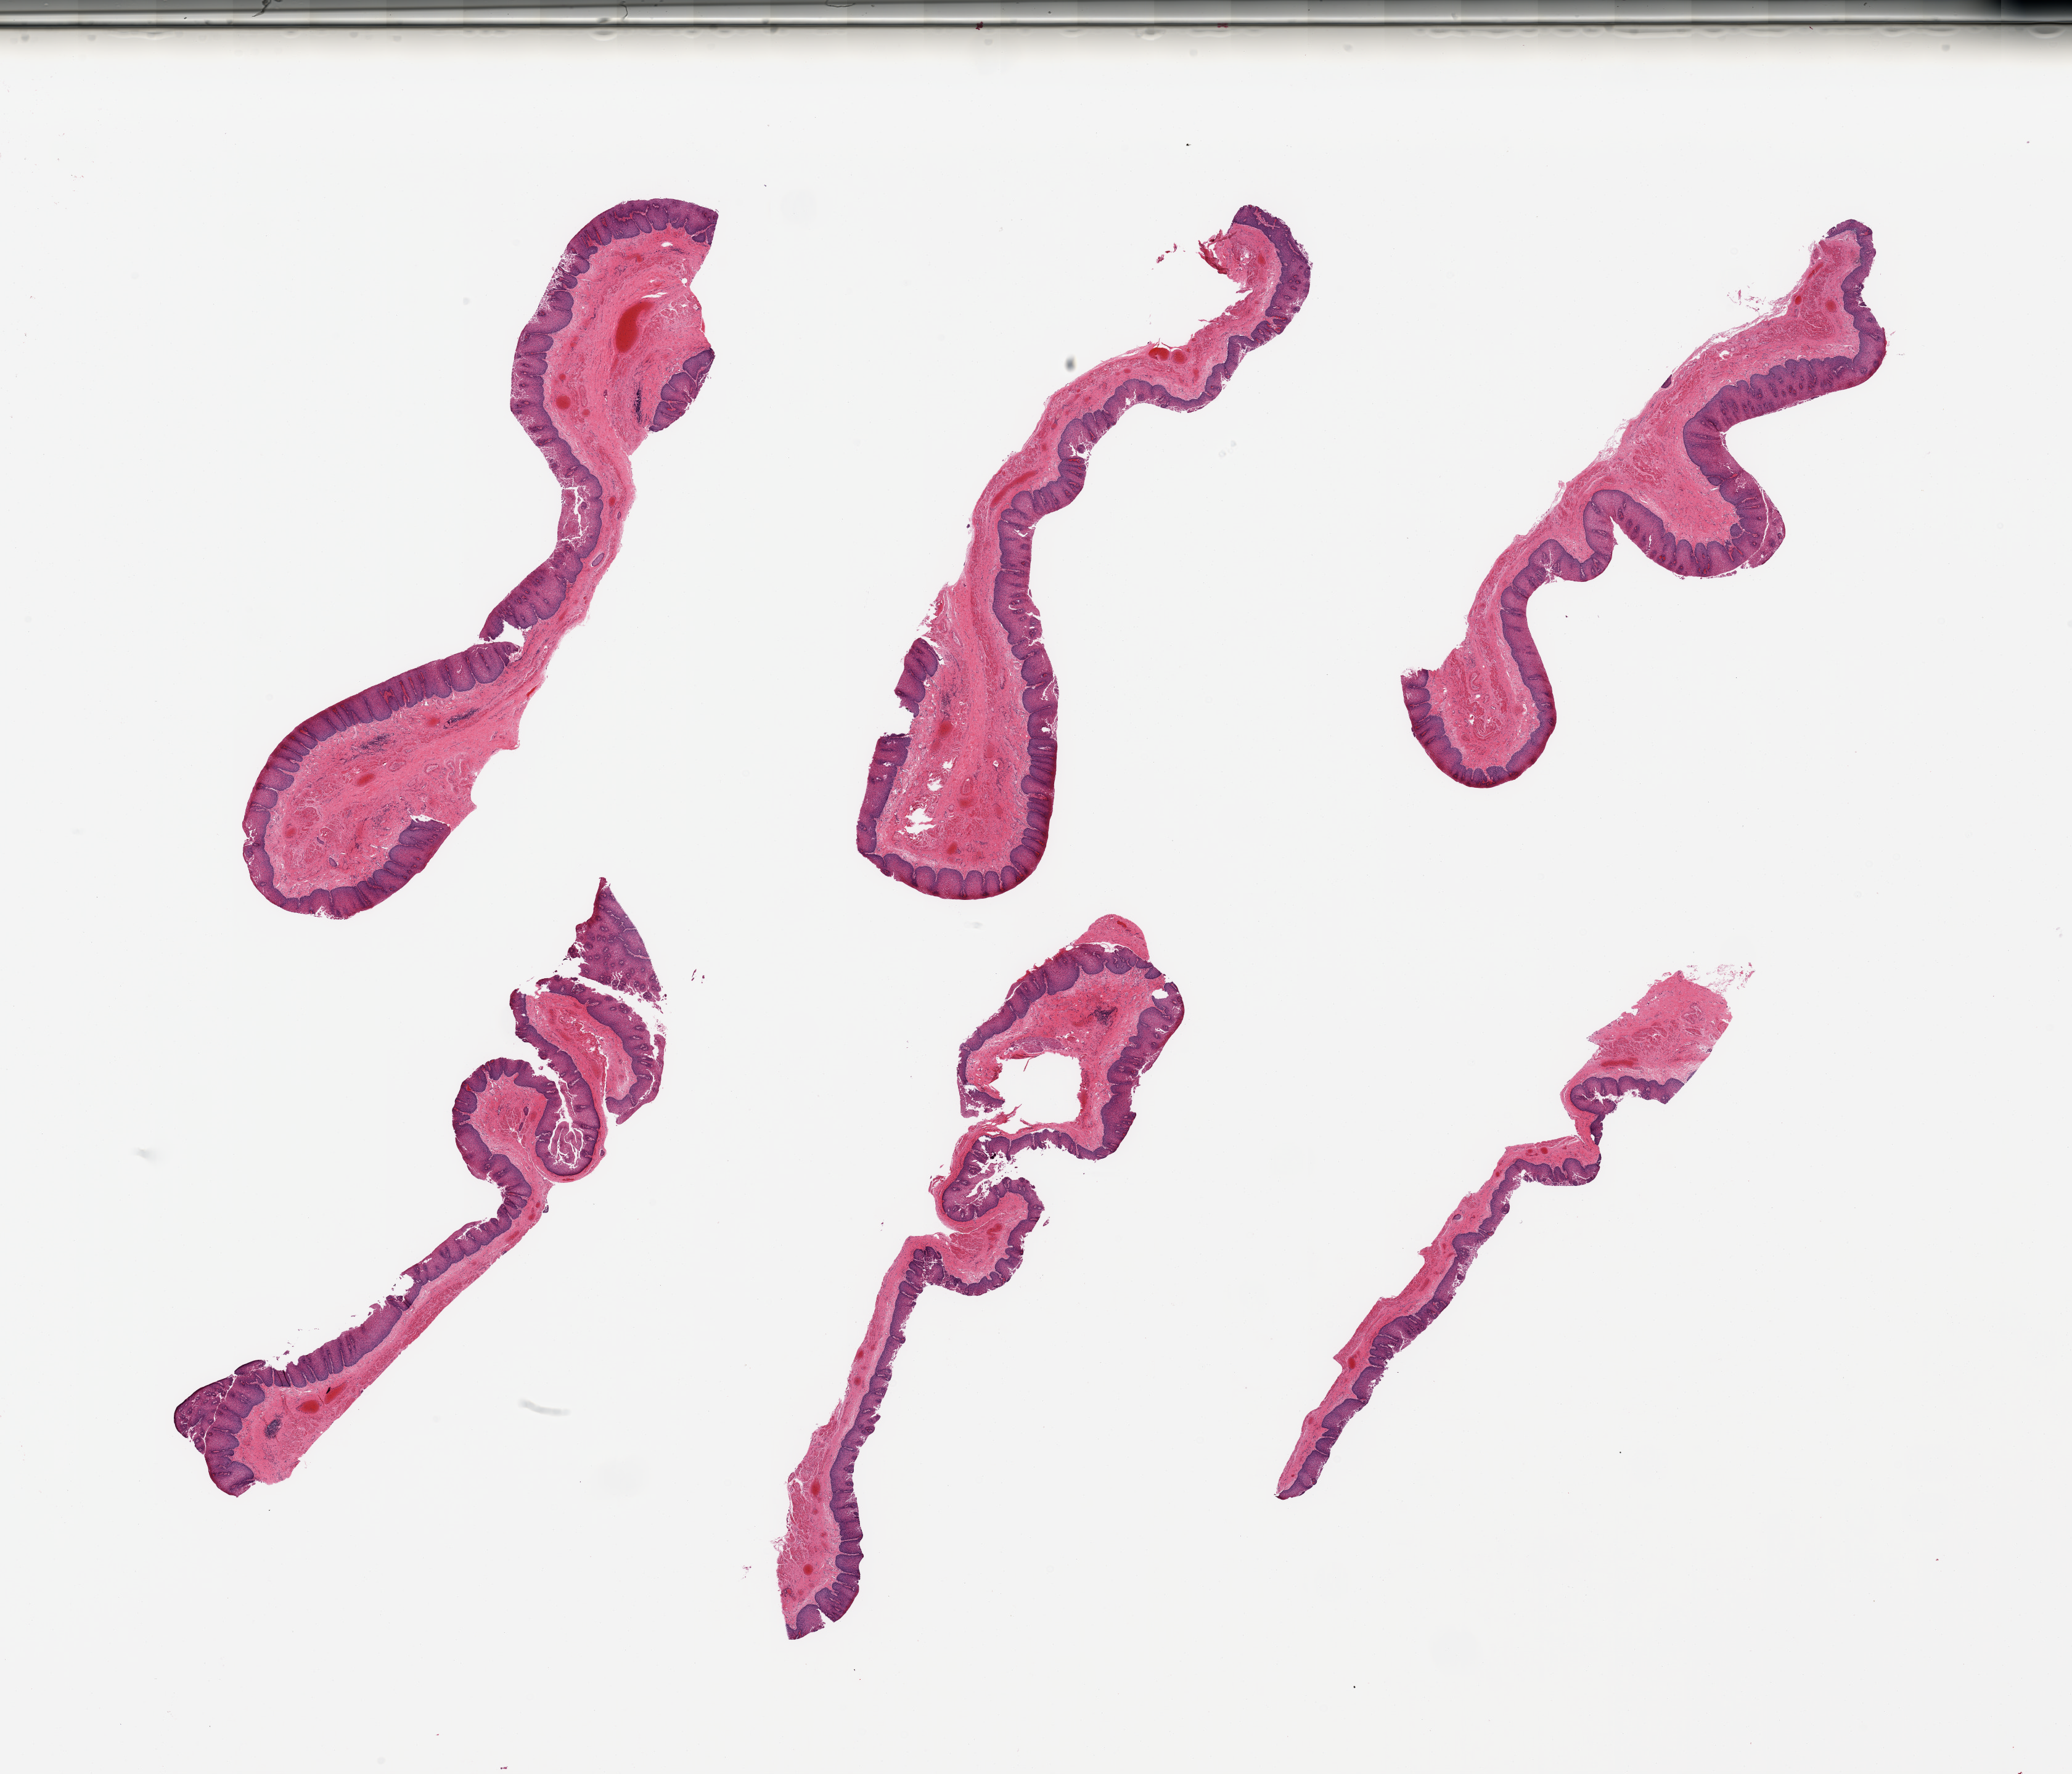
Hematoxylin and eosin (H&E) whole-slide image — shown as a low-resolution overview of the whole scanned area (about 26.6 x 22.8 mm, from a 20x scan); PAXgene-fixed paraffin-embedded (PFPE) section; section of esophageal mucous membrane (target tissue); donor tissue sample. Donor sex: male.
* reviewer comment on this tissue sample: 6 pieces; squamous hyperplasia consistent with reflux; several small subepithelial lymphoid collections; partially sloughed epithelium